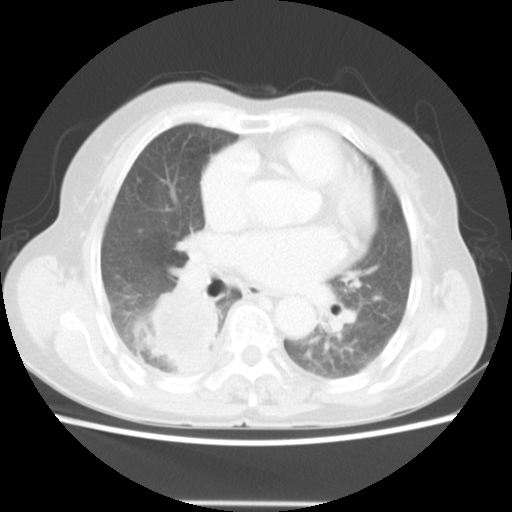
Chest CT, one axial slice. Slice 26 of 52 in the series (ordered by position). Reconstruction kernel STANDARD. Lung window (W 1500 / L -600 HU). 5 mm slice thickness. 512 × 512 image matrix, field of view 337 × 337 mm. Female patient, age 67 years. From the clinical record (not read from this slice): clinical TNM (as recorded): T3 N1 M1.
Annotated regions visible in this slice (bounding box drawn by a radiologist):
- lung tumour (recorded histology: adenocarcinoma): bounding box <139,283,223,373> (left, top, right, bottom; pixels)